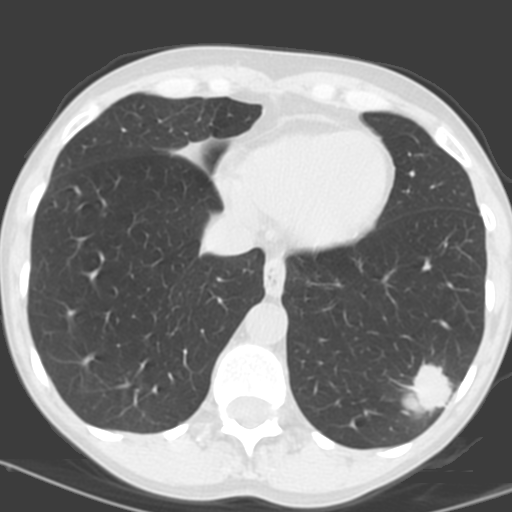
Low-dose screening chest CT, one axial slice; slice 45 of 156 in the series (ordered by position); 120 kVp; lung window (W 1500 / L -600 HU); 512 × 512 image matrix.
Annotated regions visible in this slice (outlined manually by an expert reader):
- lesion 1 (tumor, lower lobe of left lung): bounding box (x1, y1, x2, y2) in pixels: (403, 364, 451, 414)